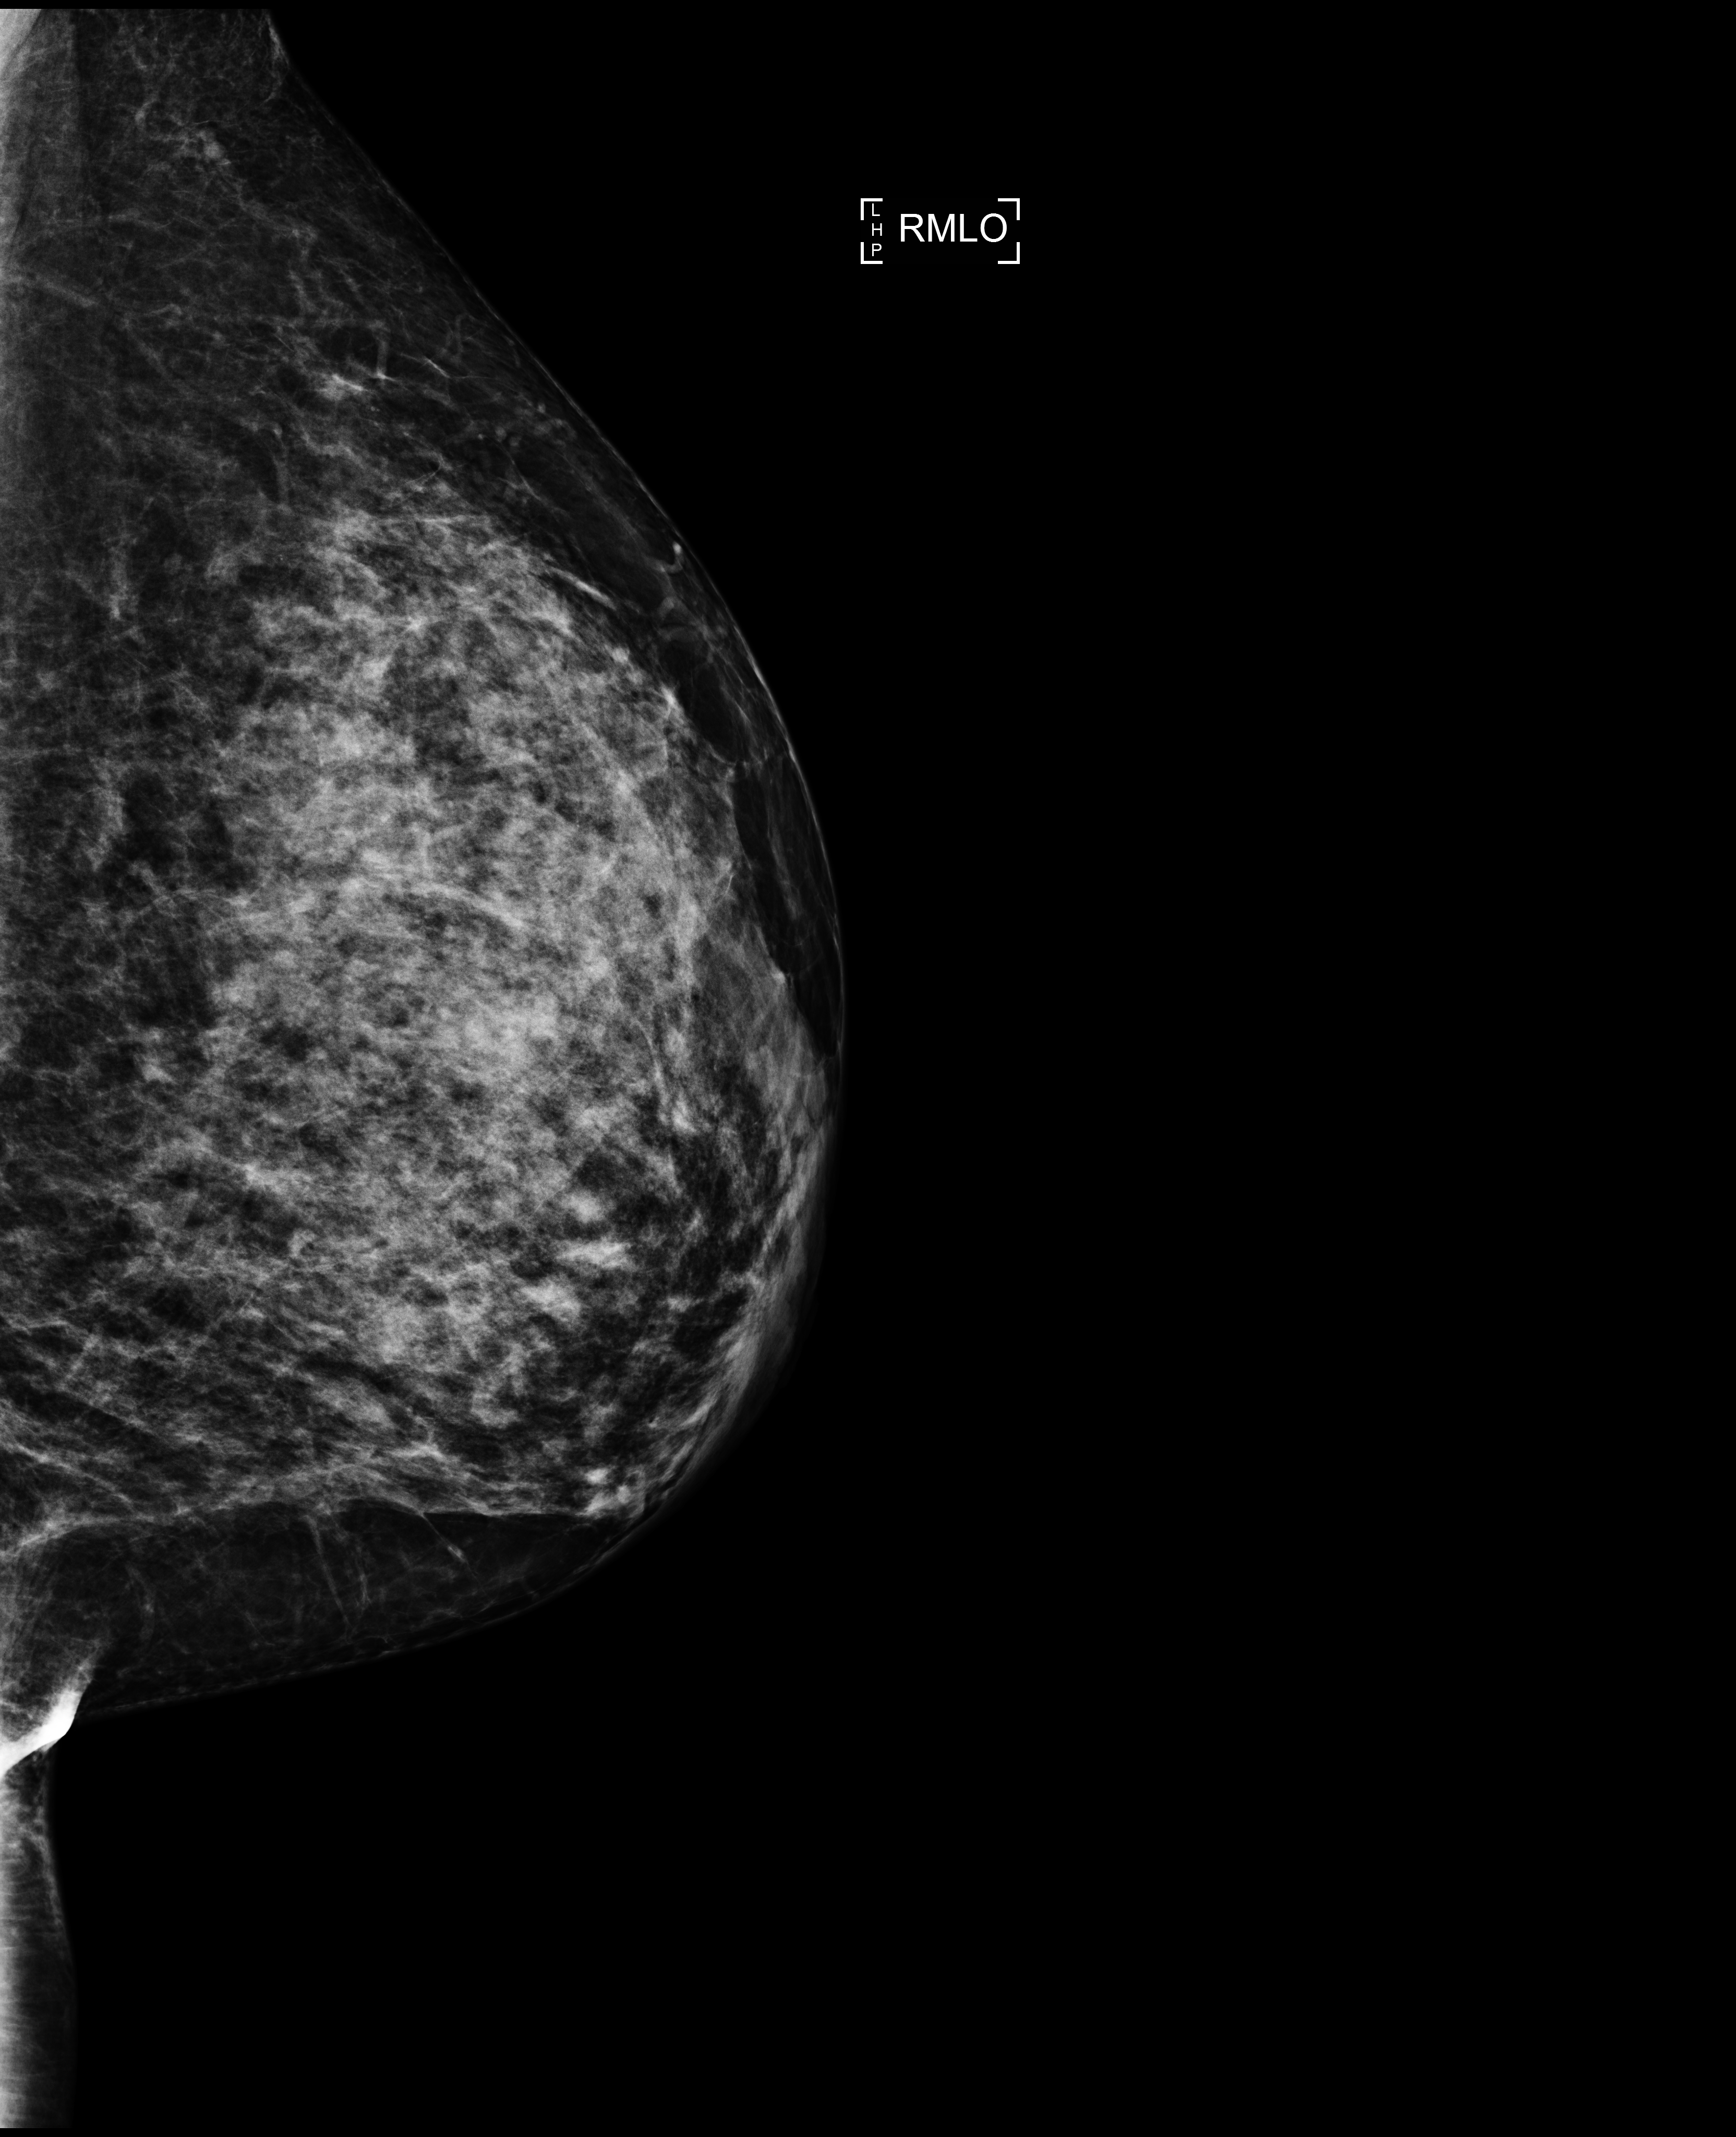
Full-field digital mammogram (FFDM), right breast, medio-lateral oblique projection, annual screening mammography examination, compressed breast thickness 73 mm, system: Selenia Dimensions. Female patient, age 42 years.
- BI-RADS breast density category at the screening exam (both breasts, scale 1–4): 3
- final BI-RADS category for the screening round (tomosynthesis exam, both breasts): category 1
- recall: no recall after this screen